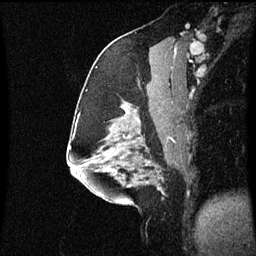
Breast MRI (dynamic contrast-enhanced), one sagittal slice; position 30 of 60 along the scan axis; dynamic contrast-enhanced series, image 2 of 3 at this slice position (ordered by acquisition); 1.5 T; TE 4.2 ms, TR 8.9 ms; 2 mm slice thickness; 256 × 256 image matrix, field of view 200 × 200 mm. Female patient, age 58 years. Case-level facts recorded for this patient, not image findings: setting: breast cancer imaged before/during neoadjuvant chemotherapy; receptor status: triple-negative.
Outlined on this slice (semi-automatically segmented with operator editing):
- analysis volume of interest (the breast-tissue region the enhancement analysis was run in; not a lesion): bounding box (x1, y1, x2, y2) in pixels: (104, 118, 171, 179)
- tumour enhancement mask (voxels above the 70 % enhancement threshold inside the analysis volume of interest): (116, 120, 141, 175)